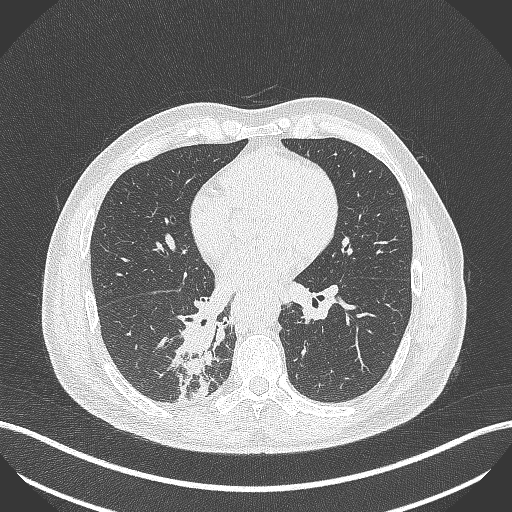
Chest CT, one axial slice; slice 215 of 451 in the series (ordered by position); reconstruction kernel B70f; lung window (W 1500 / L -600 HU); 512 × 512 image matrix, field of view 400 × 400 mm. Patient: male, 61 years. From the clinical record (not read from this slice): clinical TNM (as recorded): T1 N0 M0.
Outlined on this slice (rectangle marked by the reading radiologist):
- lung tumour (recorded histology: small cell carcinoma): bounding box <175,314,225,407> (left, top, right, bottom; pixels)